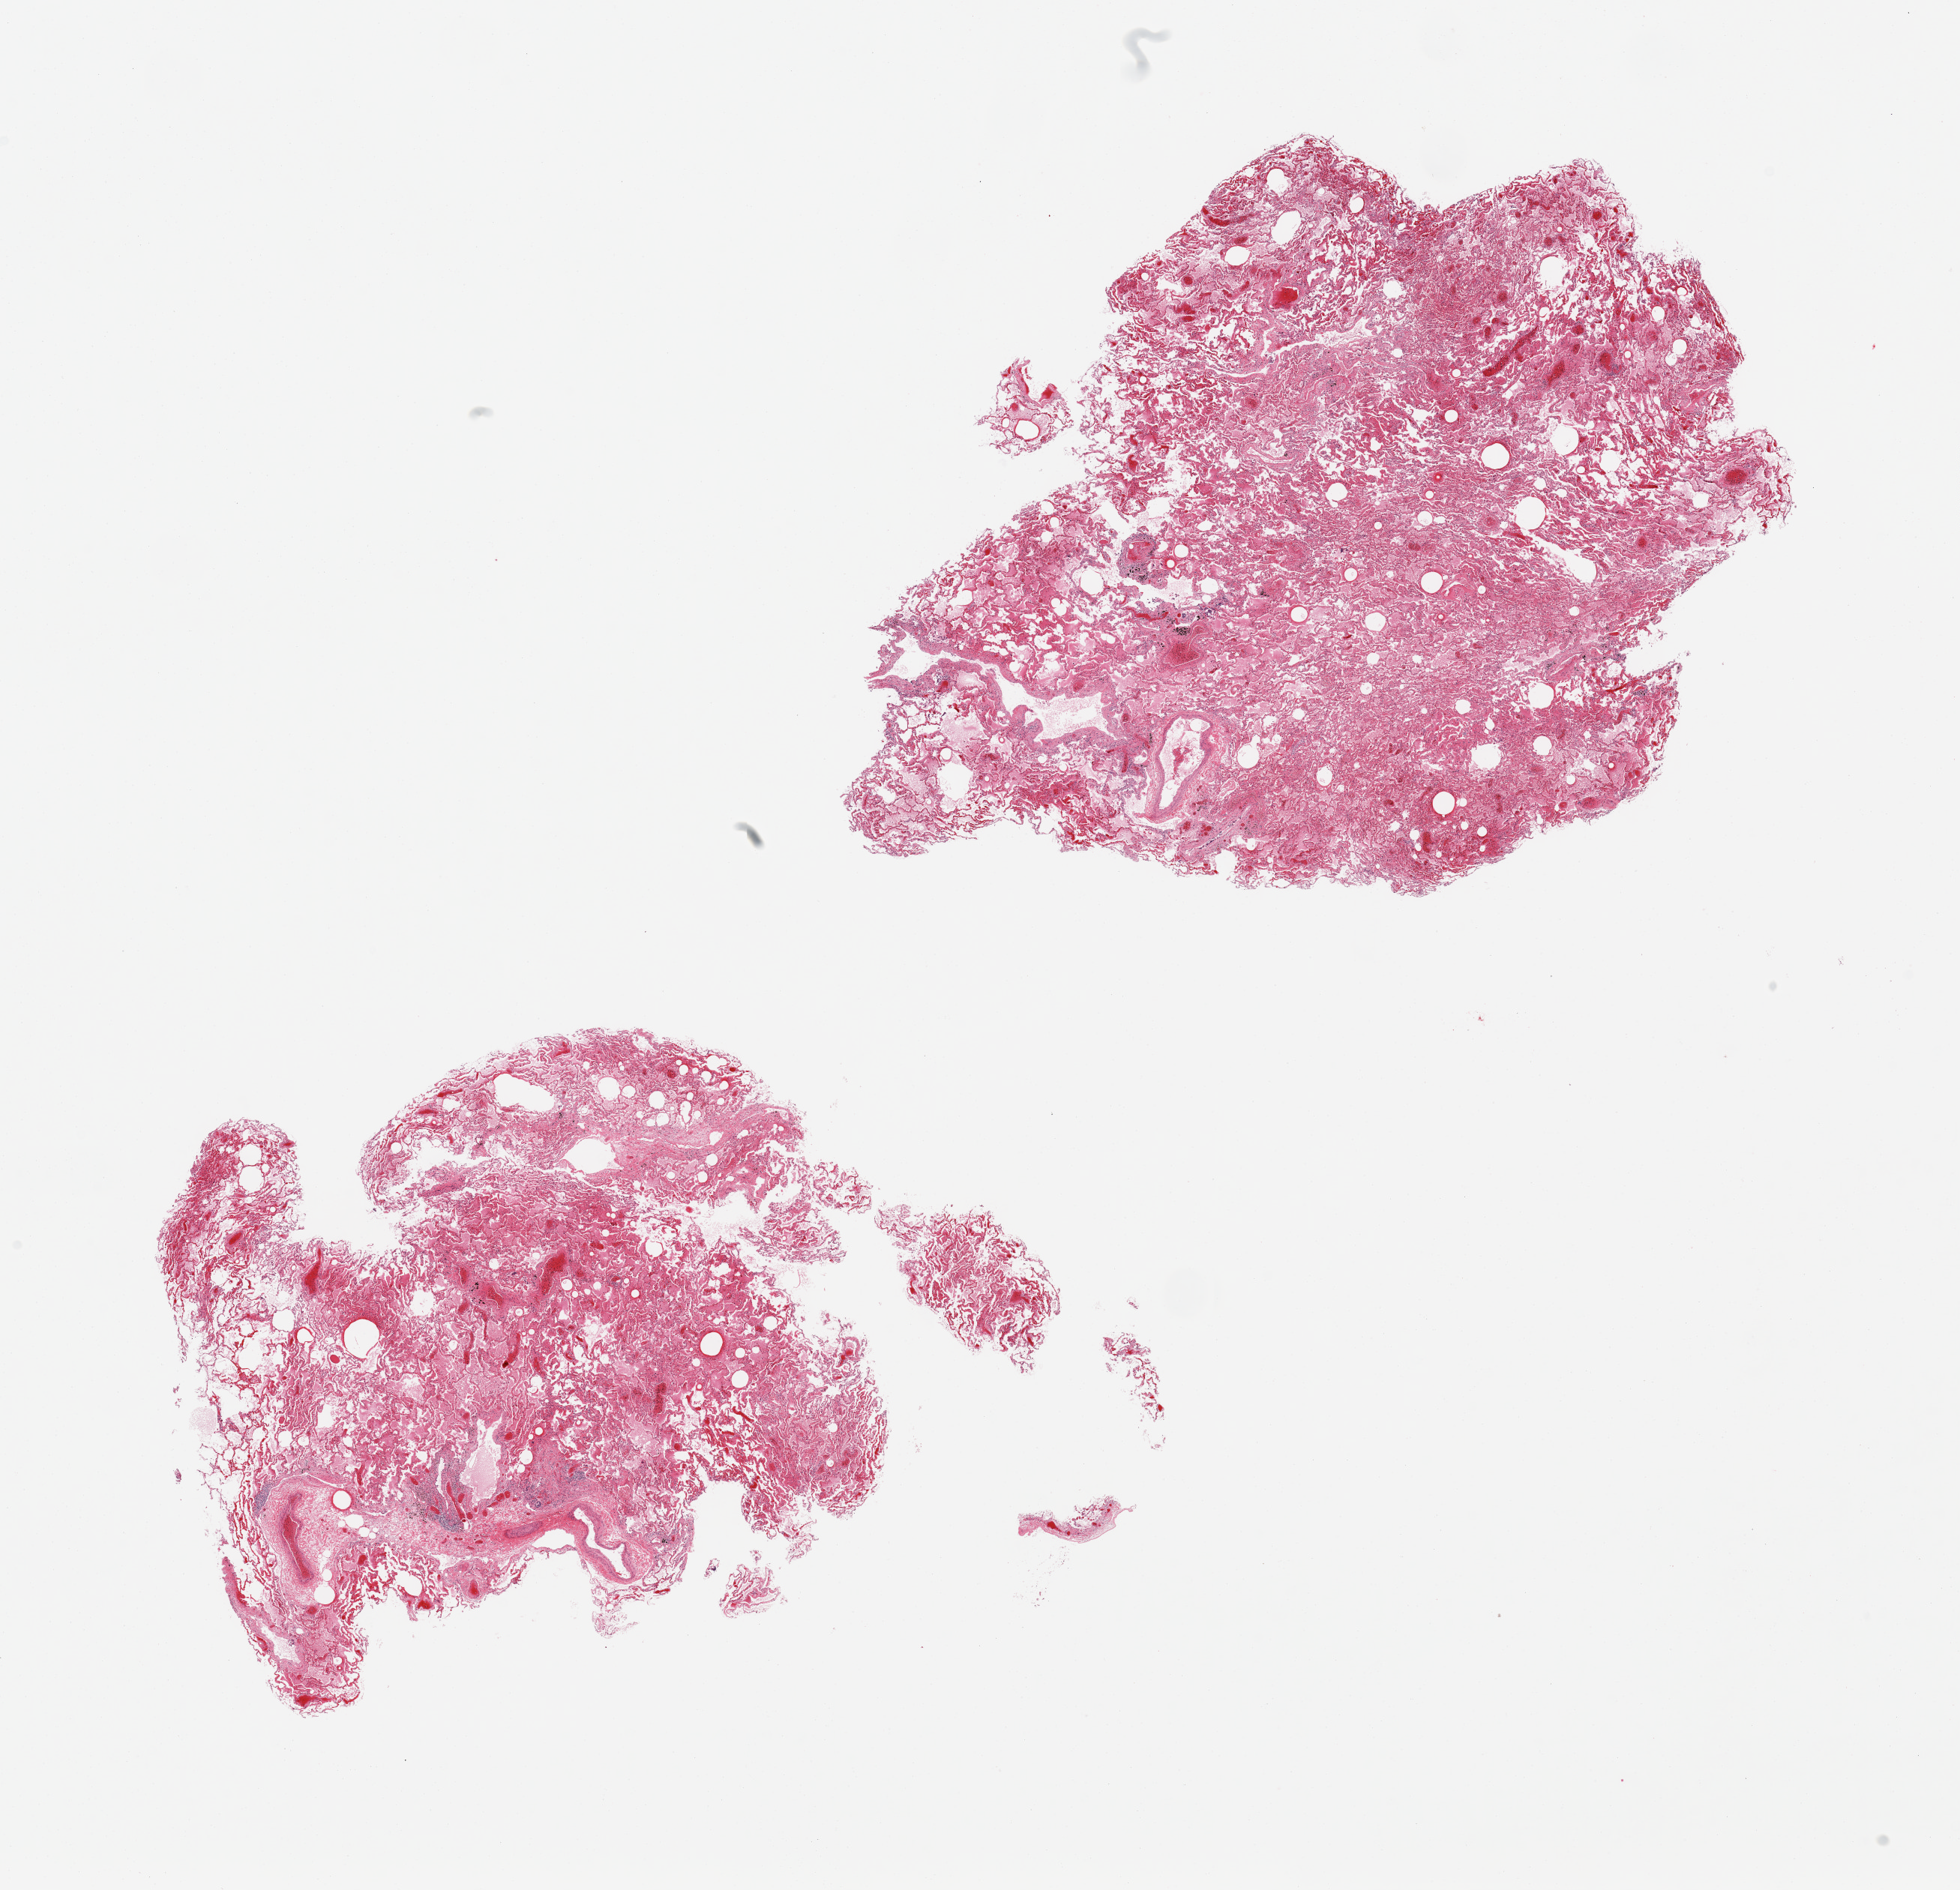
Hematoxylin and eosin (H&E) whole-slide image, brightfield, a low-resolution overview of the entire scanned area, about 20.7 x 19.9 mm (acquisition: 20x scan). PAXgene-fixed paraffin-embedded (PFPE) section. Target tissue: lung. Donor tissue sample. Female donor.
Review note (as recorded): 2 pieces mild-moderate congestion/atalectasis.